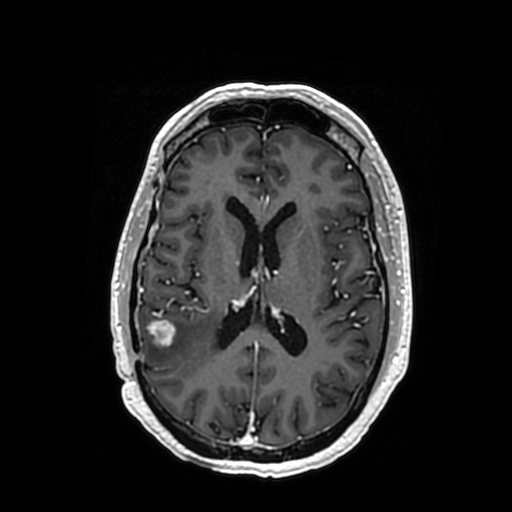
Brain MRI from a brain-tumour surgery series, one axial slice; position 163 of 364 along the scan axis; T1-weighted post-contrast; 0.5 mm slice thickness; 512 × 512 image matrix, field of view 260 × 260 mm. Case-level facts recorded for this patient, not image findings: histopathology: Oligodendroglioma; WHO grade: 3; IDH mutation: yes; tumour location: Right Posterior Temporal Inferior Parietal.
Structures marked on this image (outlined manually by an expert reader):
- tumour: bounding box [x1, y1, x2, y2] px = [157, 319, 185, 346]